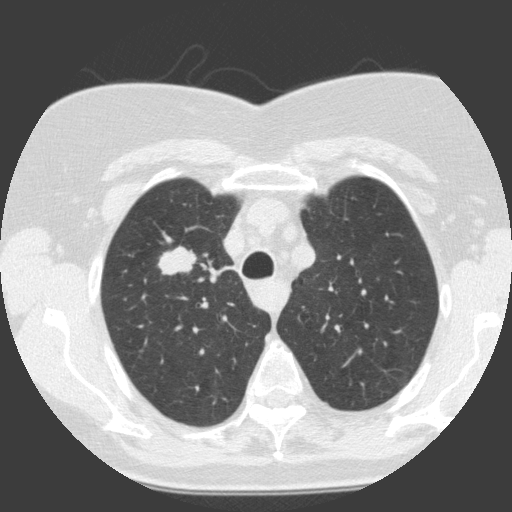
Low-dose screening chest CT, one axial slice. Slice 113 of 146 in the series (ordered by position). 120 kVp. Lung window (W 1500 / L -600 HU). 2 mm slice thickness. 512 × 512 image matrix, field of view 300 × 300 mm.
Outlined on this slice (manually delineated by an expert):
- lesion 1 (tumor, upper lobe of right lung): bounding box [x1, y1, x2, y2] px = [158, 246, 197, 276]